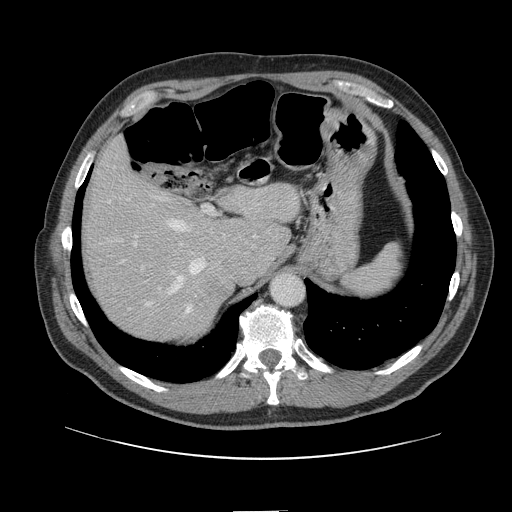
Contrast-enhanced abdominal CT, one axial slice; slice 105 of 161 in the series (ordered by position); 120 kVp; intravenous contrast given; soft-tissue window (W 400 / L 40 HU); 2.5 mm slice thickness; 512 × 512 image matrix. Male patient, age 66 years. From the clinical record (not read from this slice): diagnosis: colorectal cancer liver metastases, imaged before liver resection; multiple liver metastases: no.
Outlined on this slice (outlined manually by an expert reader):
- hepatic veins: box from (x=109, y=200) to (x=207, y=313) px
- liver: (x=85, y=144)–(x=299, y=340)
- planned liver remnant (the part of the liver to remain after resection): (x=85, y=144)–(x=299, y=308)
- portal vein (with intrahepatic branches): (x=129, y=205)–(x=216, y=310)
- liver metastasis: (x=194, y=272)–(x=226, y=312)